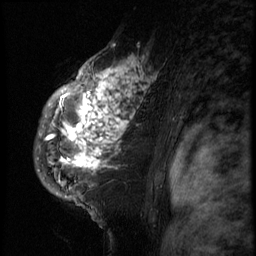
Breast MRI (dynamic contrast-enhanced), one sagittal slice. Slice 50 of 66 in the series (ordered by position). 3 images stored at this slice position (order not interpretable as contrast timing). 1.5 T. TE 4.2 ms, TR 8.9 ms. 2.5 mm slice thickness. 256 × 256 image matrix, field of view 200 × 200 mm. Patient: female, 39 years. From the clinical record (not read from this slice): setting: breast cancer imaged before/during neoadjuvant chemotherapy; receptor status: HER2-positive.
Annotated regions visible in this slice (semi-automatically segmented with operator editing):
- analysis volume of interest (the breast-tissue region the enhancement analysis was run in; not a lesion): box from (x=33, y=44) to (x=166, y=196) px
- tumour enhancement mask (voxels above the 140 % enhancement threshold inside the analysis volume of interest): (x=45, y=44)–(x=156, y=170)